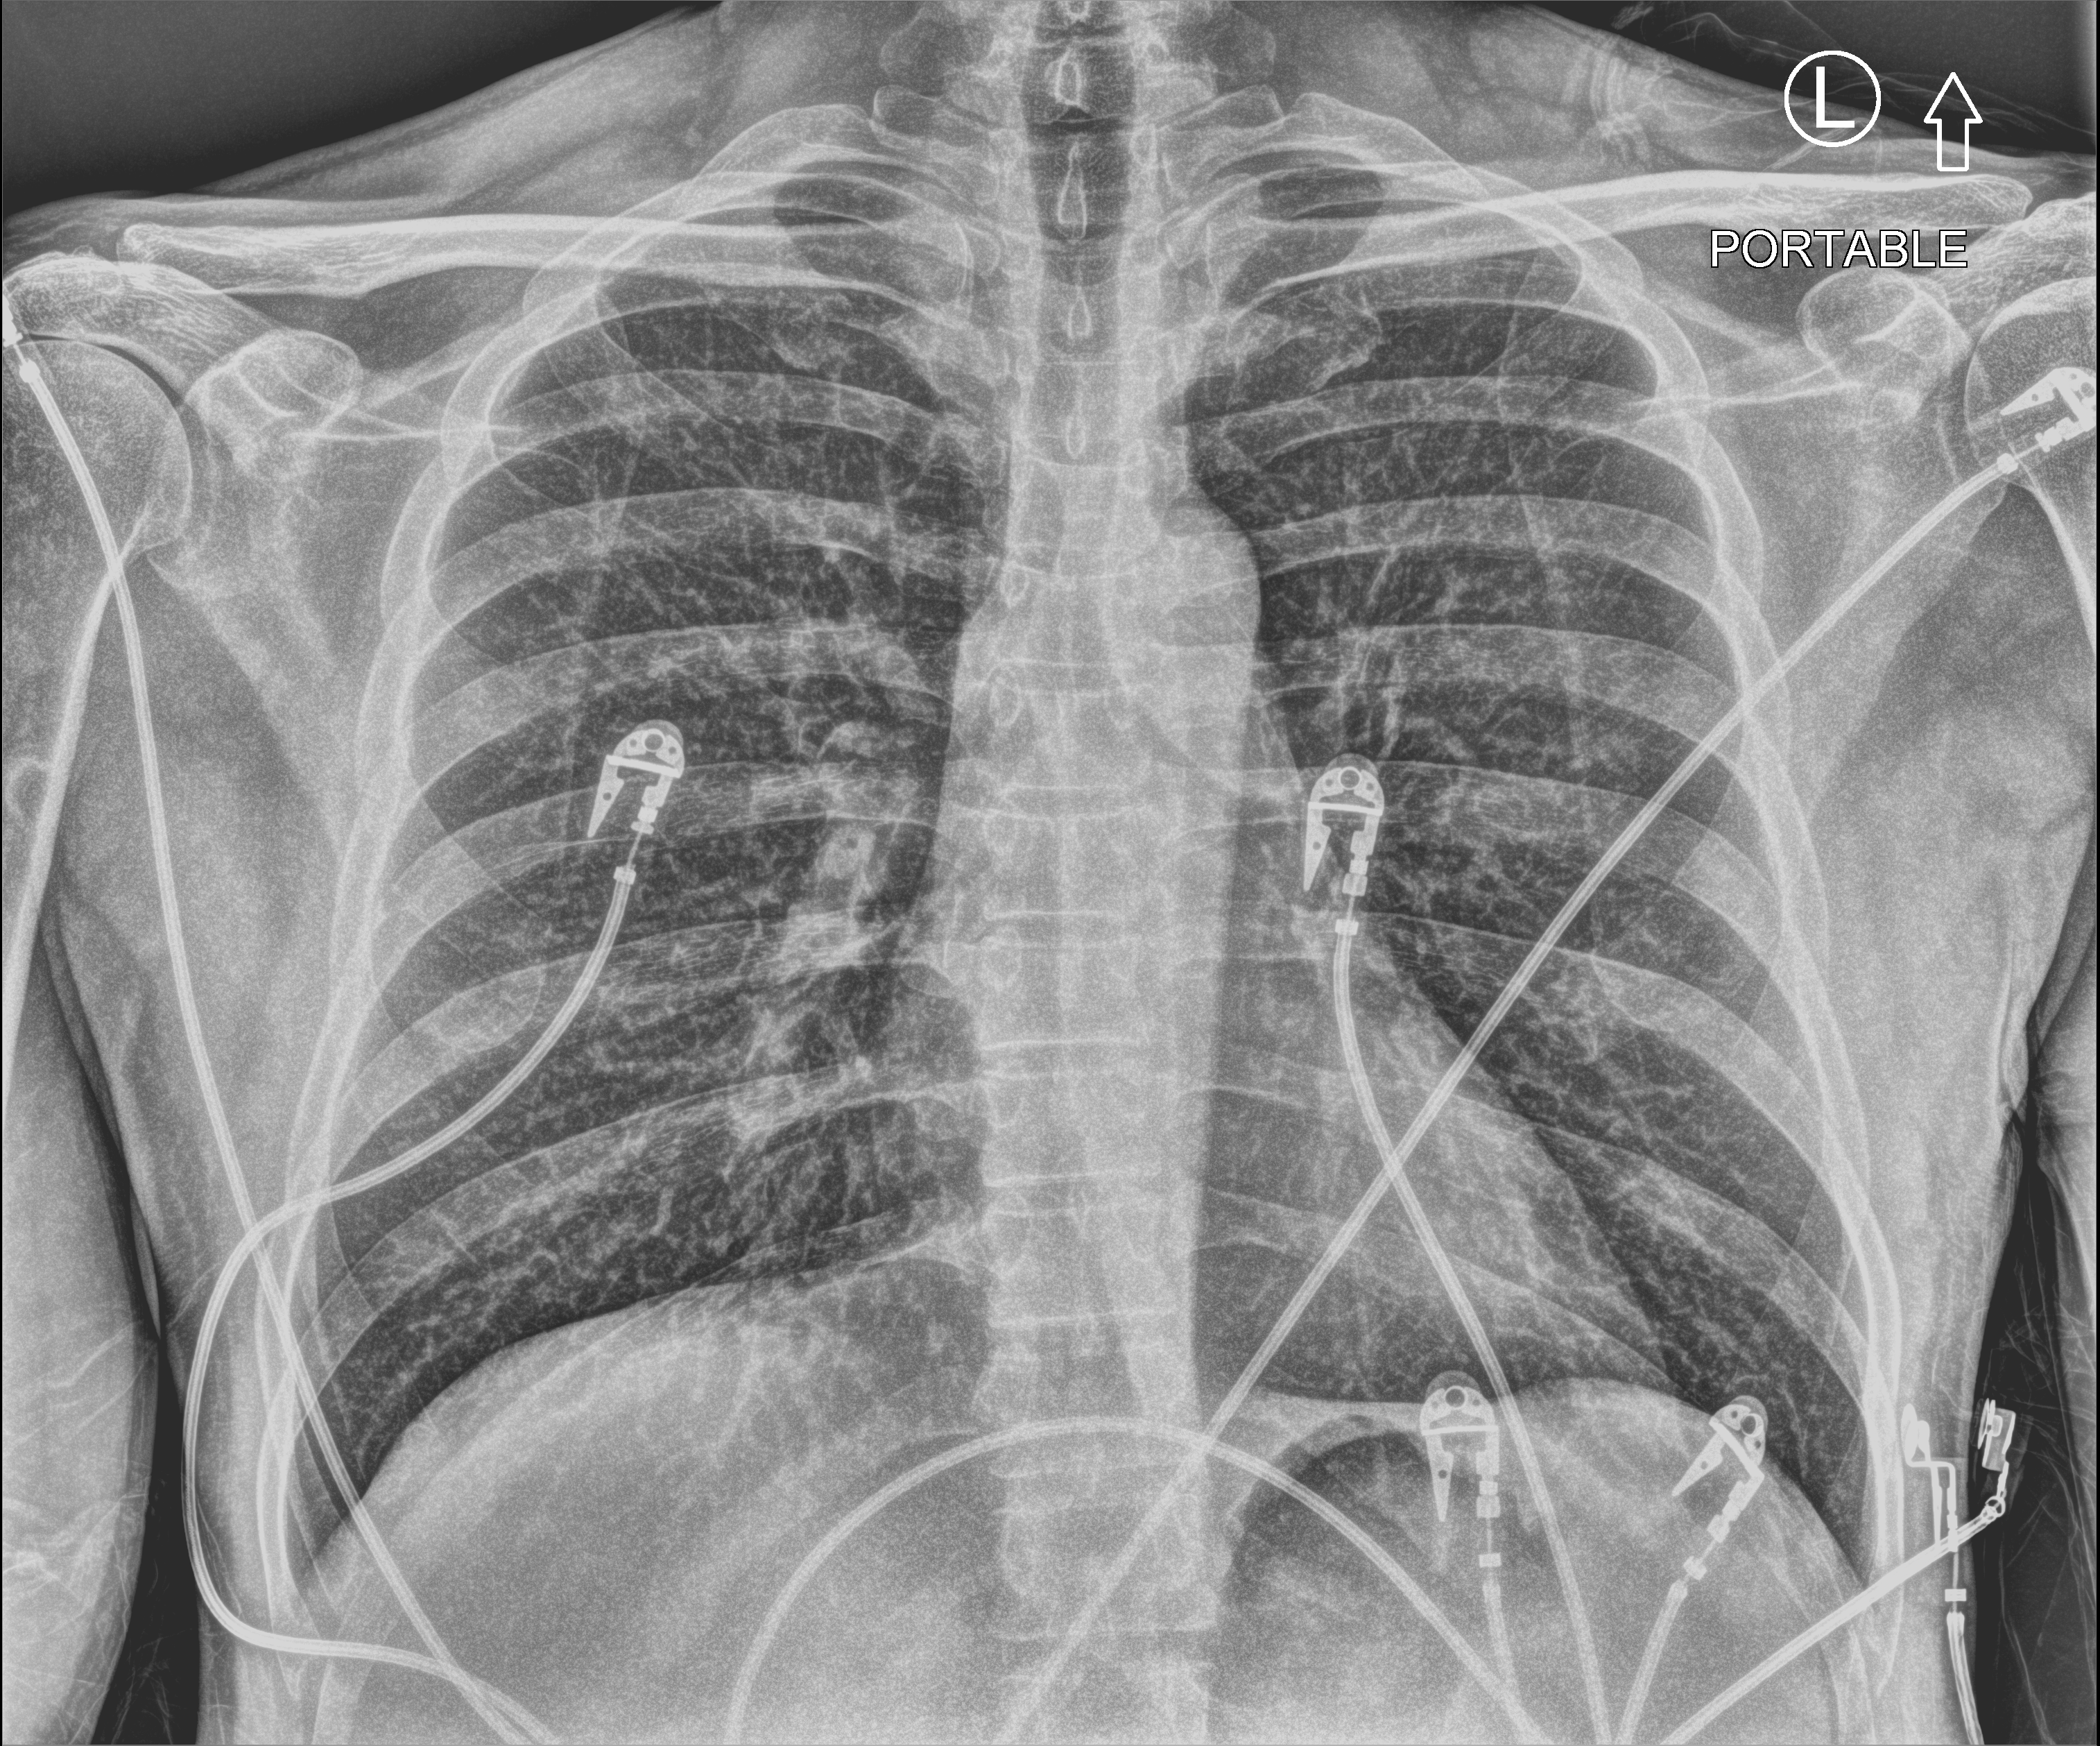
Bedside chest radiograph (computed radiography); anteroposterior (AP) projection. Male patient hospitalised with COVID-19, age 18–59 years.
Admission-level facts for this patient (not findings on this image; timing relative to this image not recorded): mechanically ventilated during this hospital stay: no; smoking status (admission record): never.